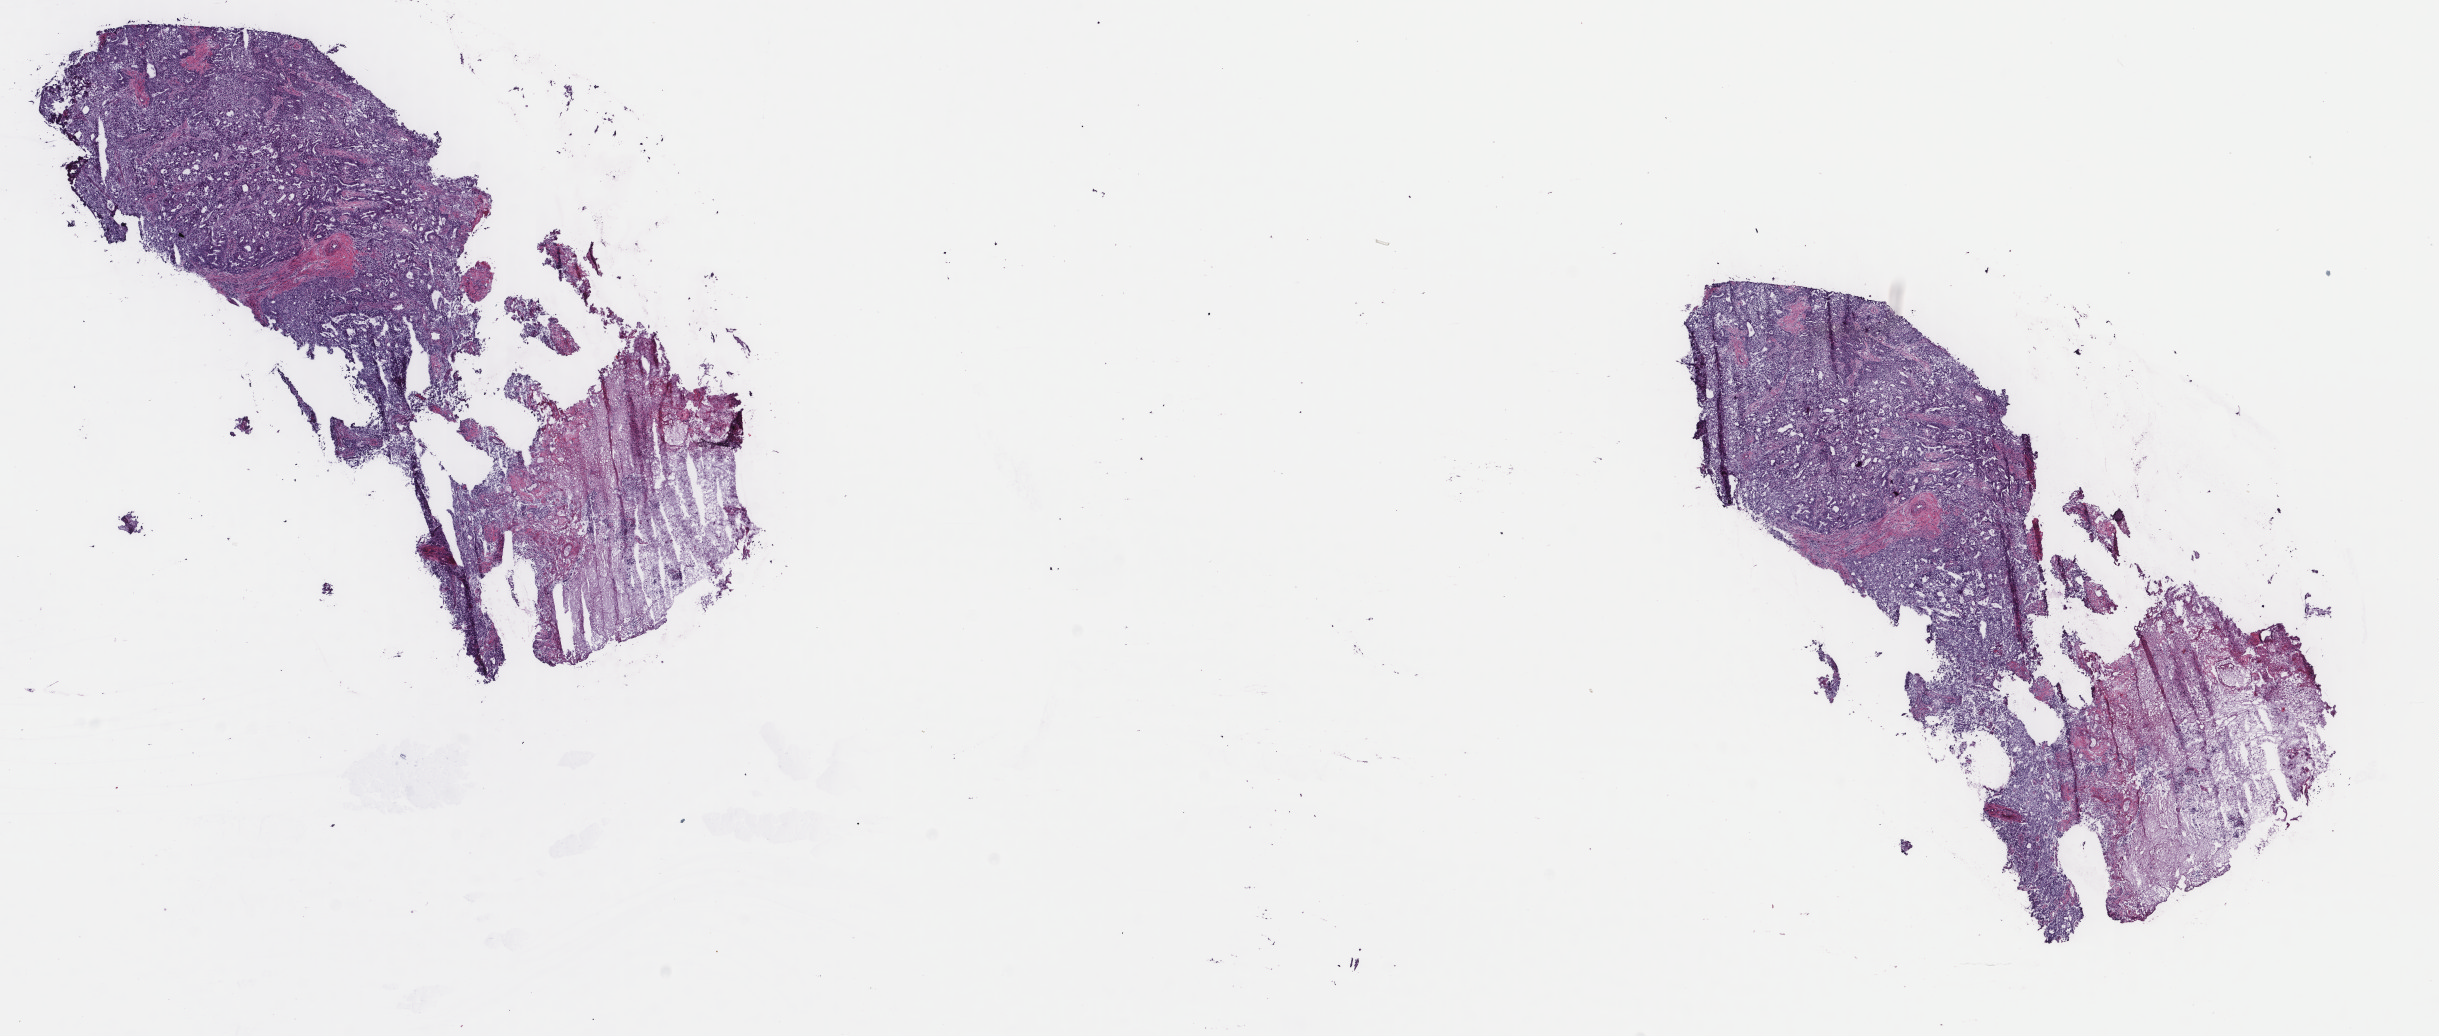
H&E whole-slide image, a low-resolution overview of the entire scanned area, about 19.4 x 8.2 mm (acquisition: 40x scan), frozen section from the top of the tissue portion, sample: primary tumour, uterus. Female patient; age at initial diagnosis 63 years. Histologic grade: G2 (moderately differentiated). Composition of this section per pathologist review: tumour cells 50%, tumour nuclei 70%, normal cells 0%, stromal cells 30%, necrosis 20%. Inflammatory infiltration, as recorded: lymphocyte infiltration 4%, monocyte infiltration 6%, neutrophil infiltration 2%.
Lymph nodes positive (case pathology): 0 of 23 examined. Histologic diagnosis: Endometrioid adenocarcinoma, NOS. FIGO stage: IV.